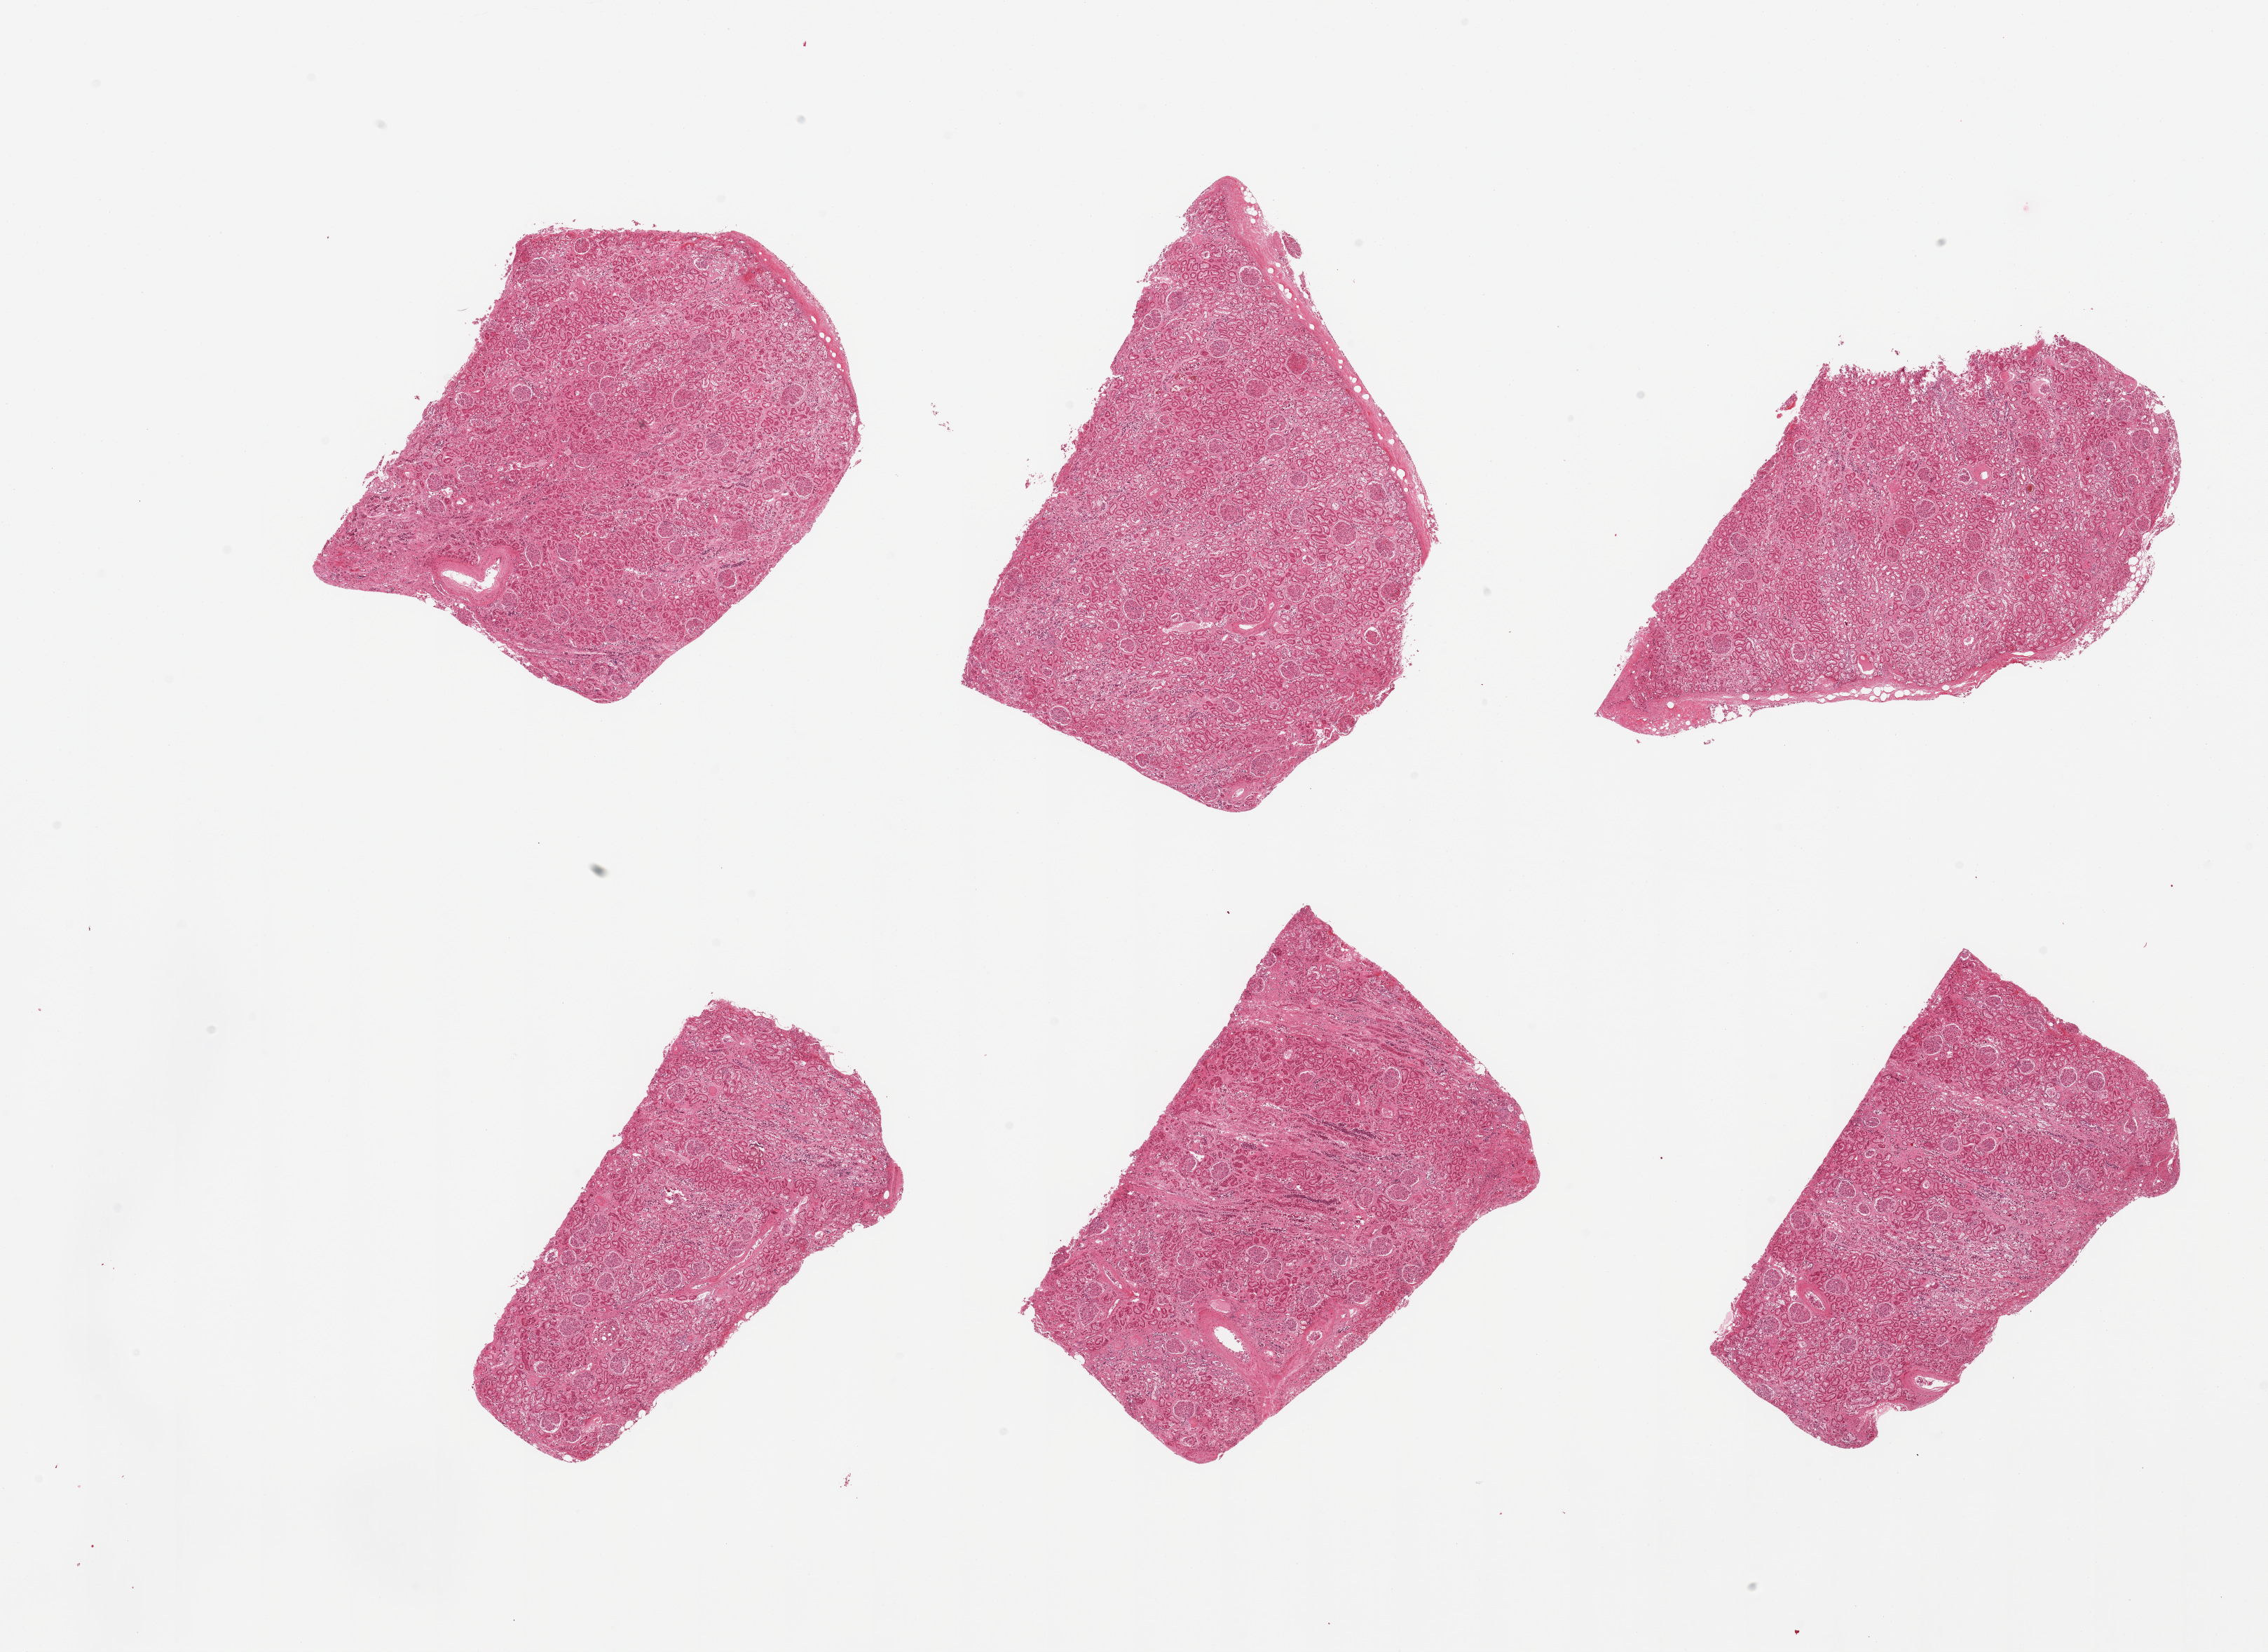
Digitized hematoxylin and eosin (H&E)-stained section — whole scanned area (about 25.6 x 18.6 mm, acquisition: 20x scan) shown as a low-resolution overview, PAXgene-fixed paraffin-embedded (PFPE) section, section of renal cortex (target tissue), tissue donor sample. Donor sex: male.
• reviewer comment on this tissue sample: 6 pieces, glomeruli present, tubular cells badly degraded/autolyzed